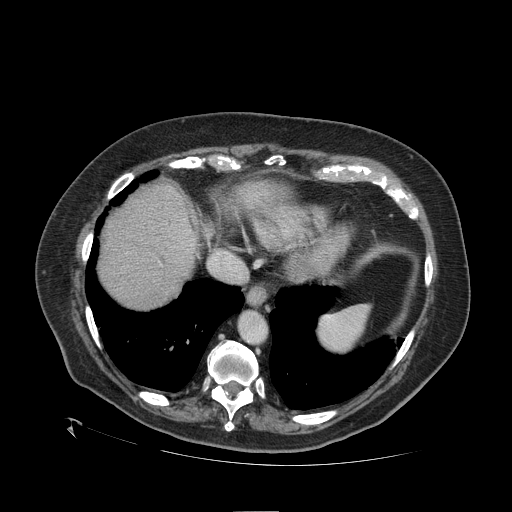
Contrast-enhanced abdominal CT (liver protocol), one axial slice. Position 93 of 109 along the scan axis. 120 kVp. One of 2 acquisitions stored at this slice position. Soft-tissue window (W 400 / L 40 HU). 2.5 mm slice thickness. 512 × 512 image matrix, field of view 460 × 460 mm. Case-level facts recorded for this patient, not image findings: diagnosis: hepatocellular carcinoma (patient treated with transarterial chemoembolisation; whether this scan precedes or follows treatment is not stated here); TNM stage (as recorded): Stage-I; Child-Pugh class: A; tumour differentiation: no biopsy; tumour nodularity: uninodular.
Outlined on this slice (semi-automatically segmented with operator editing):
- abdominal aorta: bounding box [x1, y1, x2, y2] px = [240, 313, 266, 343]
- liver parenchyma outside the tumour (the mass and vessels are separate outlines, so this box may not span the whole liver): [100, 182, 198, 308]